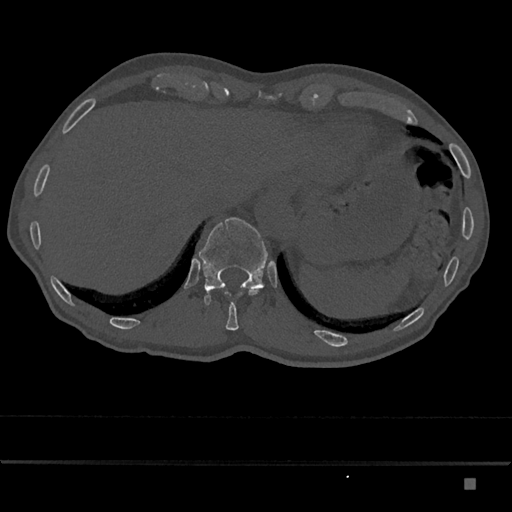
CT including the spine, one axial slice. Position 641 of 797 along the scan axis. Bone window (W 1800 / L 400 HU). 0.5 mm slice thickness. 512 × 512 image matrix, field of view 390 × 390 mm. Patient: male, 72 years. From the clinical record (not read from this slice): primary cancer: prostate.
Structures marked on this image (semi-automatically segmented with operator editing):
- T11 vertebra: box from (x=226, y=289) to (x=257, y=330) px
- T12 vertebra: (x=199, y=217)–(x=268, y=305)